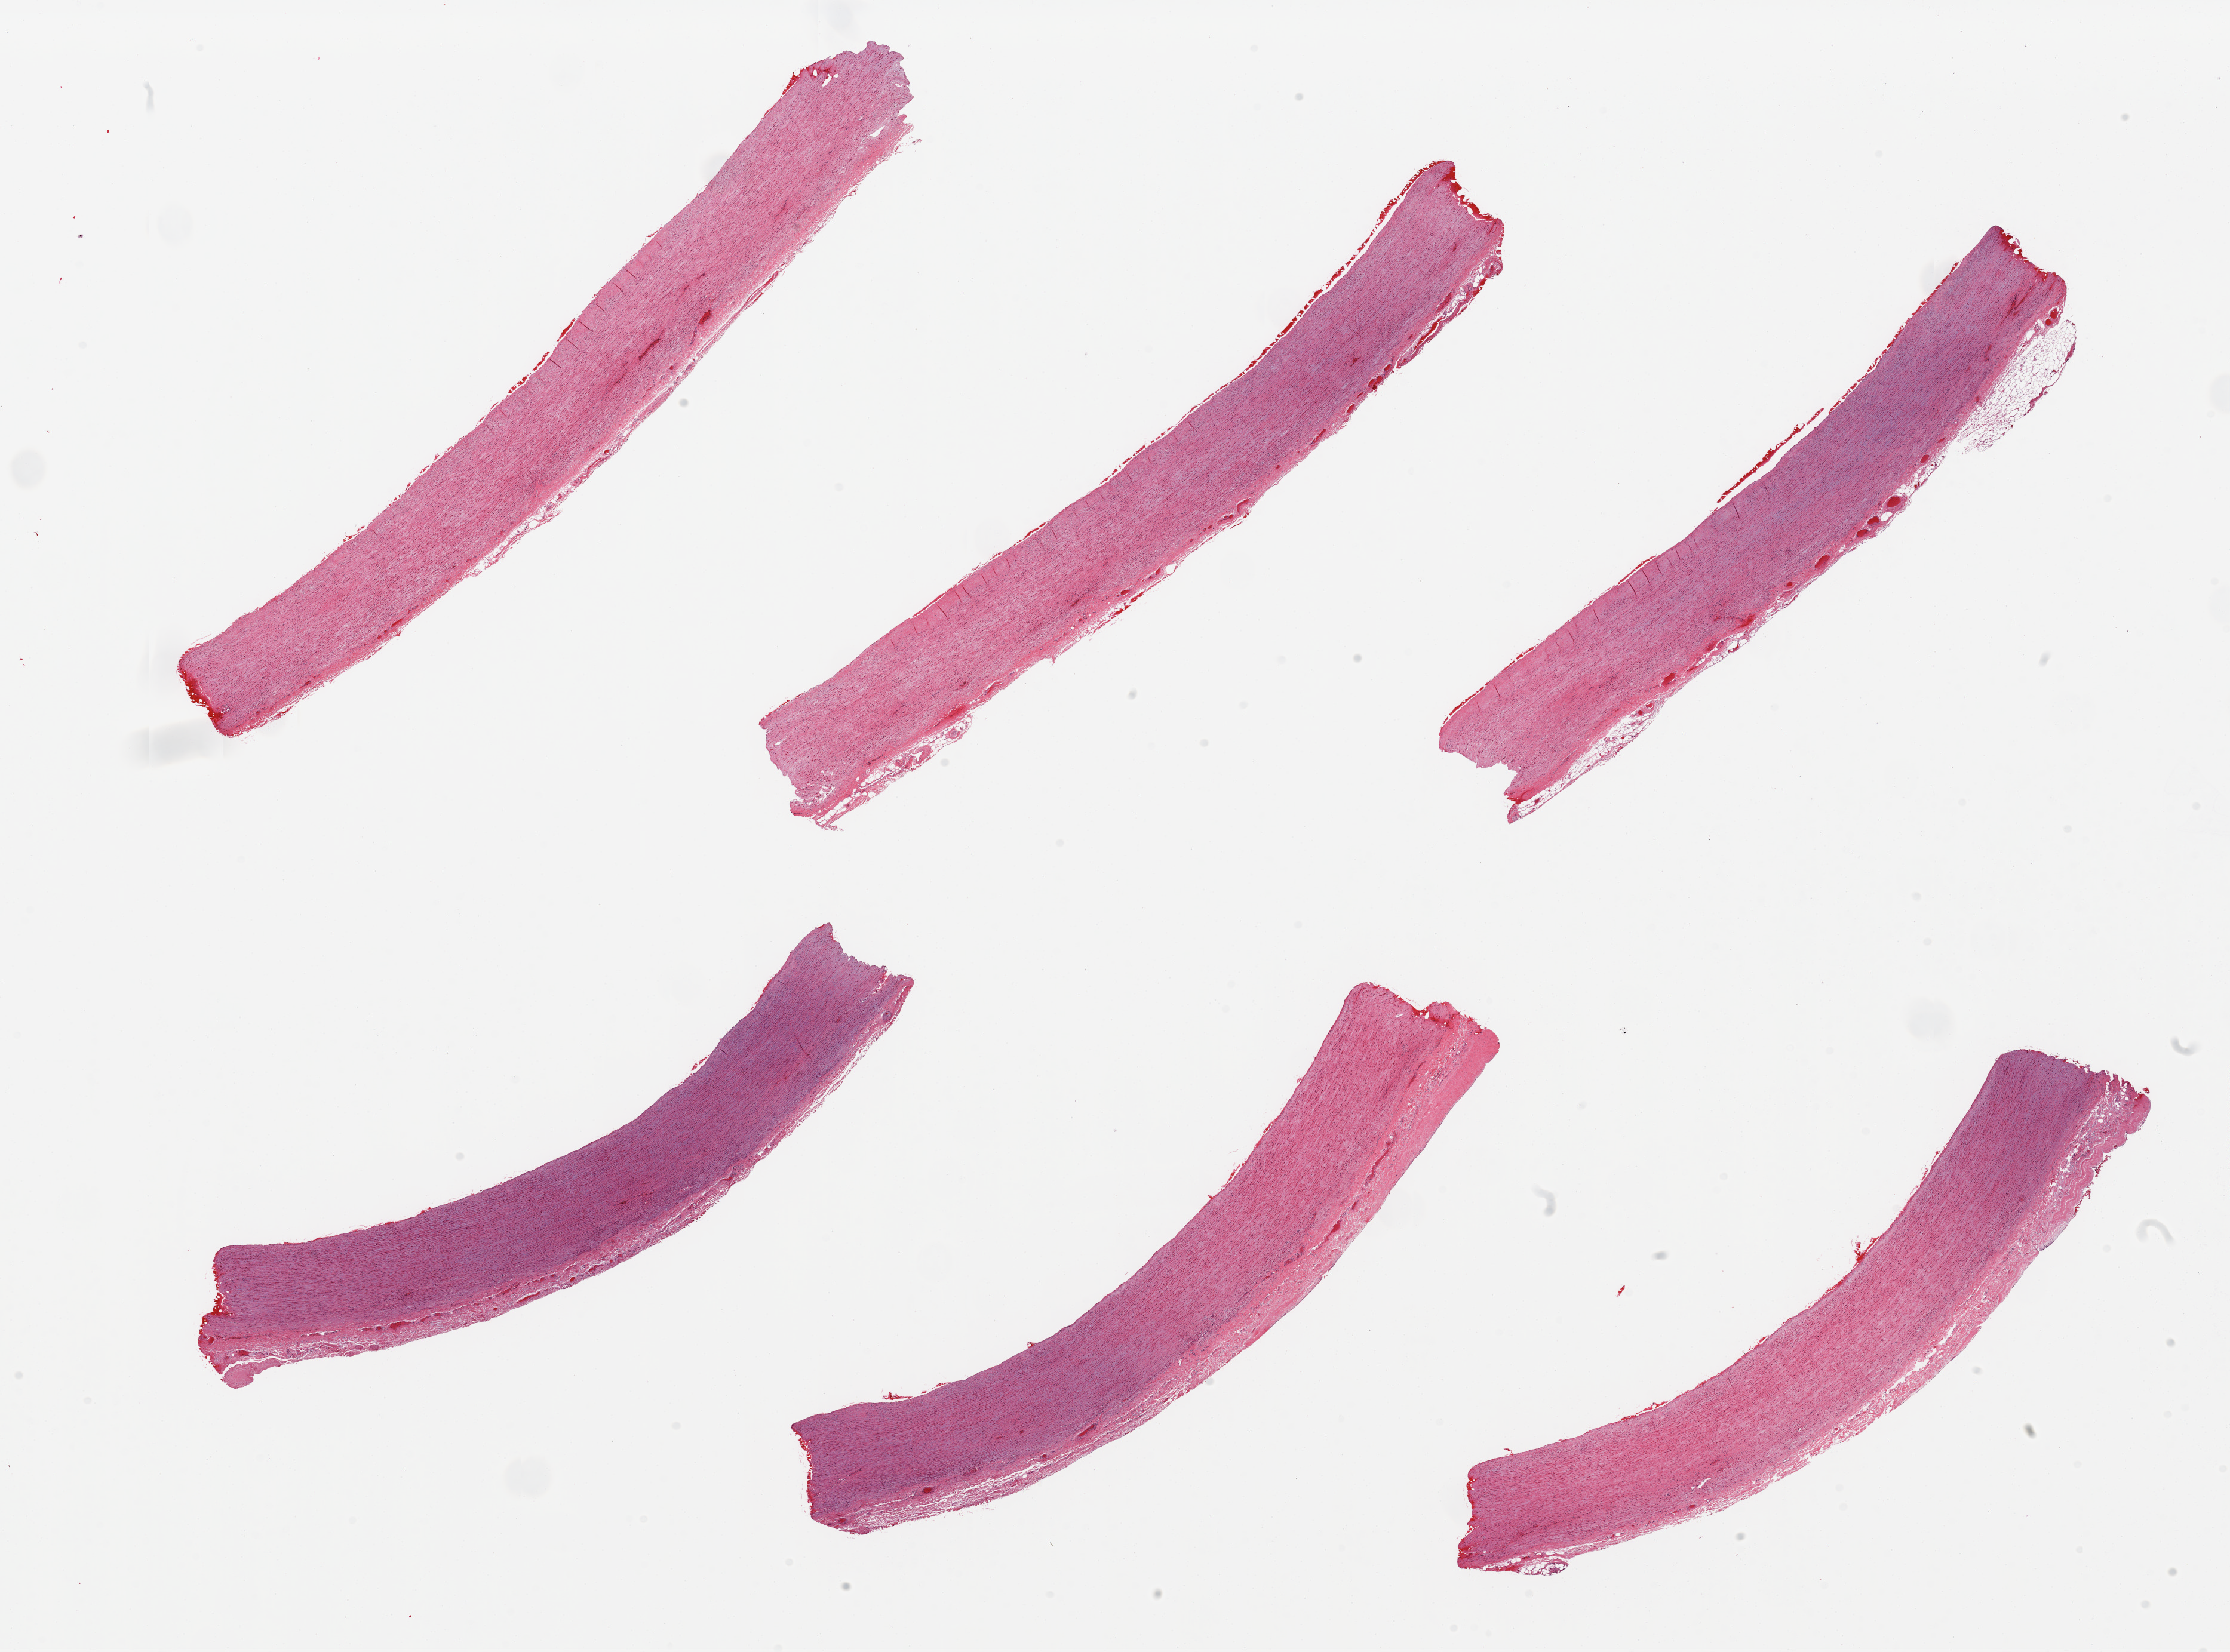
Digitized hematoxylin and eosin (H&E)-stained section, brightfield, shown as a low-resolution overview of the whole scanned area (about 29.5 x 21.9 mm, slide scanned at 20x); PAXgene-fixed, paraffin-embedded tissue; sampled site (target tissue): aorta; donor tissue sample. Male donor.
Review note (as recorded): 6 pieces; well trimmed.